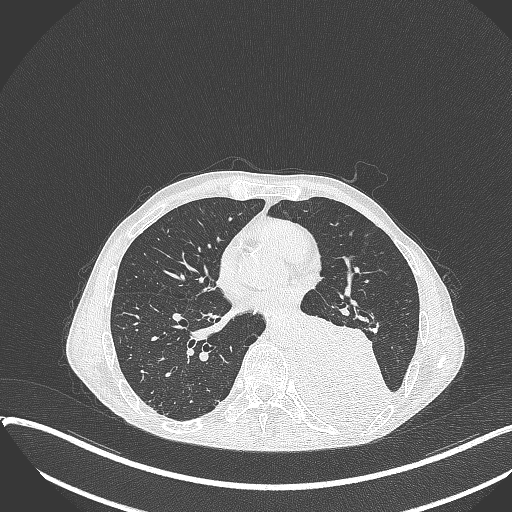
Chest CT, one axial slice. Reconstruction kernel B70f. Lung window (W 1500 / L -600 HU). 512 × 512 image matrix. Patient: male, 57 years. From the clinical record (not read from this slice): clinical TNM (as recorded): T4 N0 M0.
Structures marked on this image (bounding box drawn by a radiologist):
- lung tumour (recorded histology: squamous cell carcinoma): bounding box <287,305,397,428> (left, top, right, bottom; pixels)